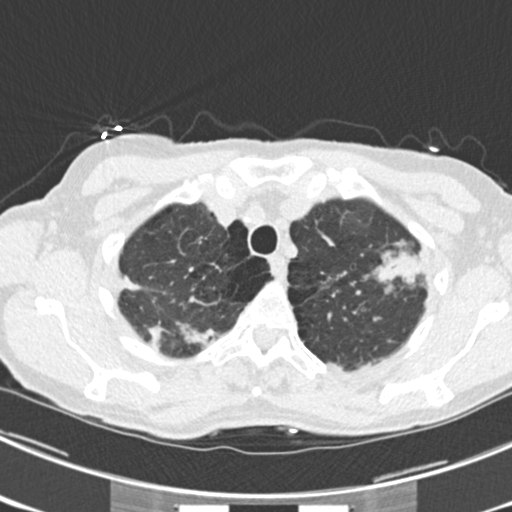
Chest CT (low-dose screening protocol), one axial image; third annual screen; lung window (W 1500 / L -600 HU); slice 41 of 225 in the series. Female, age 63 years at enrolment. Current smoker at enrolment.
Expert-annotated lung lesion, box from (x=373, y=238) to (x=440, y=301) px. The screening reader recorded 9 non-calcified nodules or masses ≥4 mm on this exam (left upper lobe, right upper lobe, left upper lobe, left lower lobe, right middle lobe, left lower lobe, left lower lobe, right lower lobe, right lower lobe); which of them this box marks is not recorded. Lung cancer was diagnosed 15 days after this screen: bronchiolo-alveolar adenocarcinoma, NOS, right upper lobe, right middle lobe, right lower lobe, left upper lobe, left lower lobe, moderately differentiated (G2), stage IV (AJCC 6th edition).